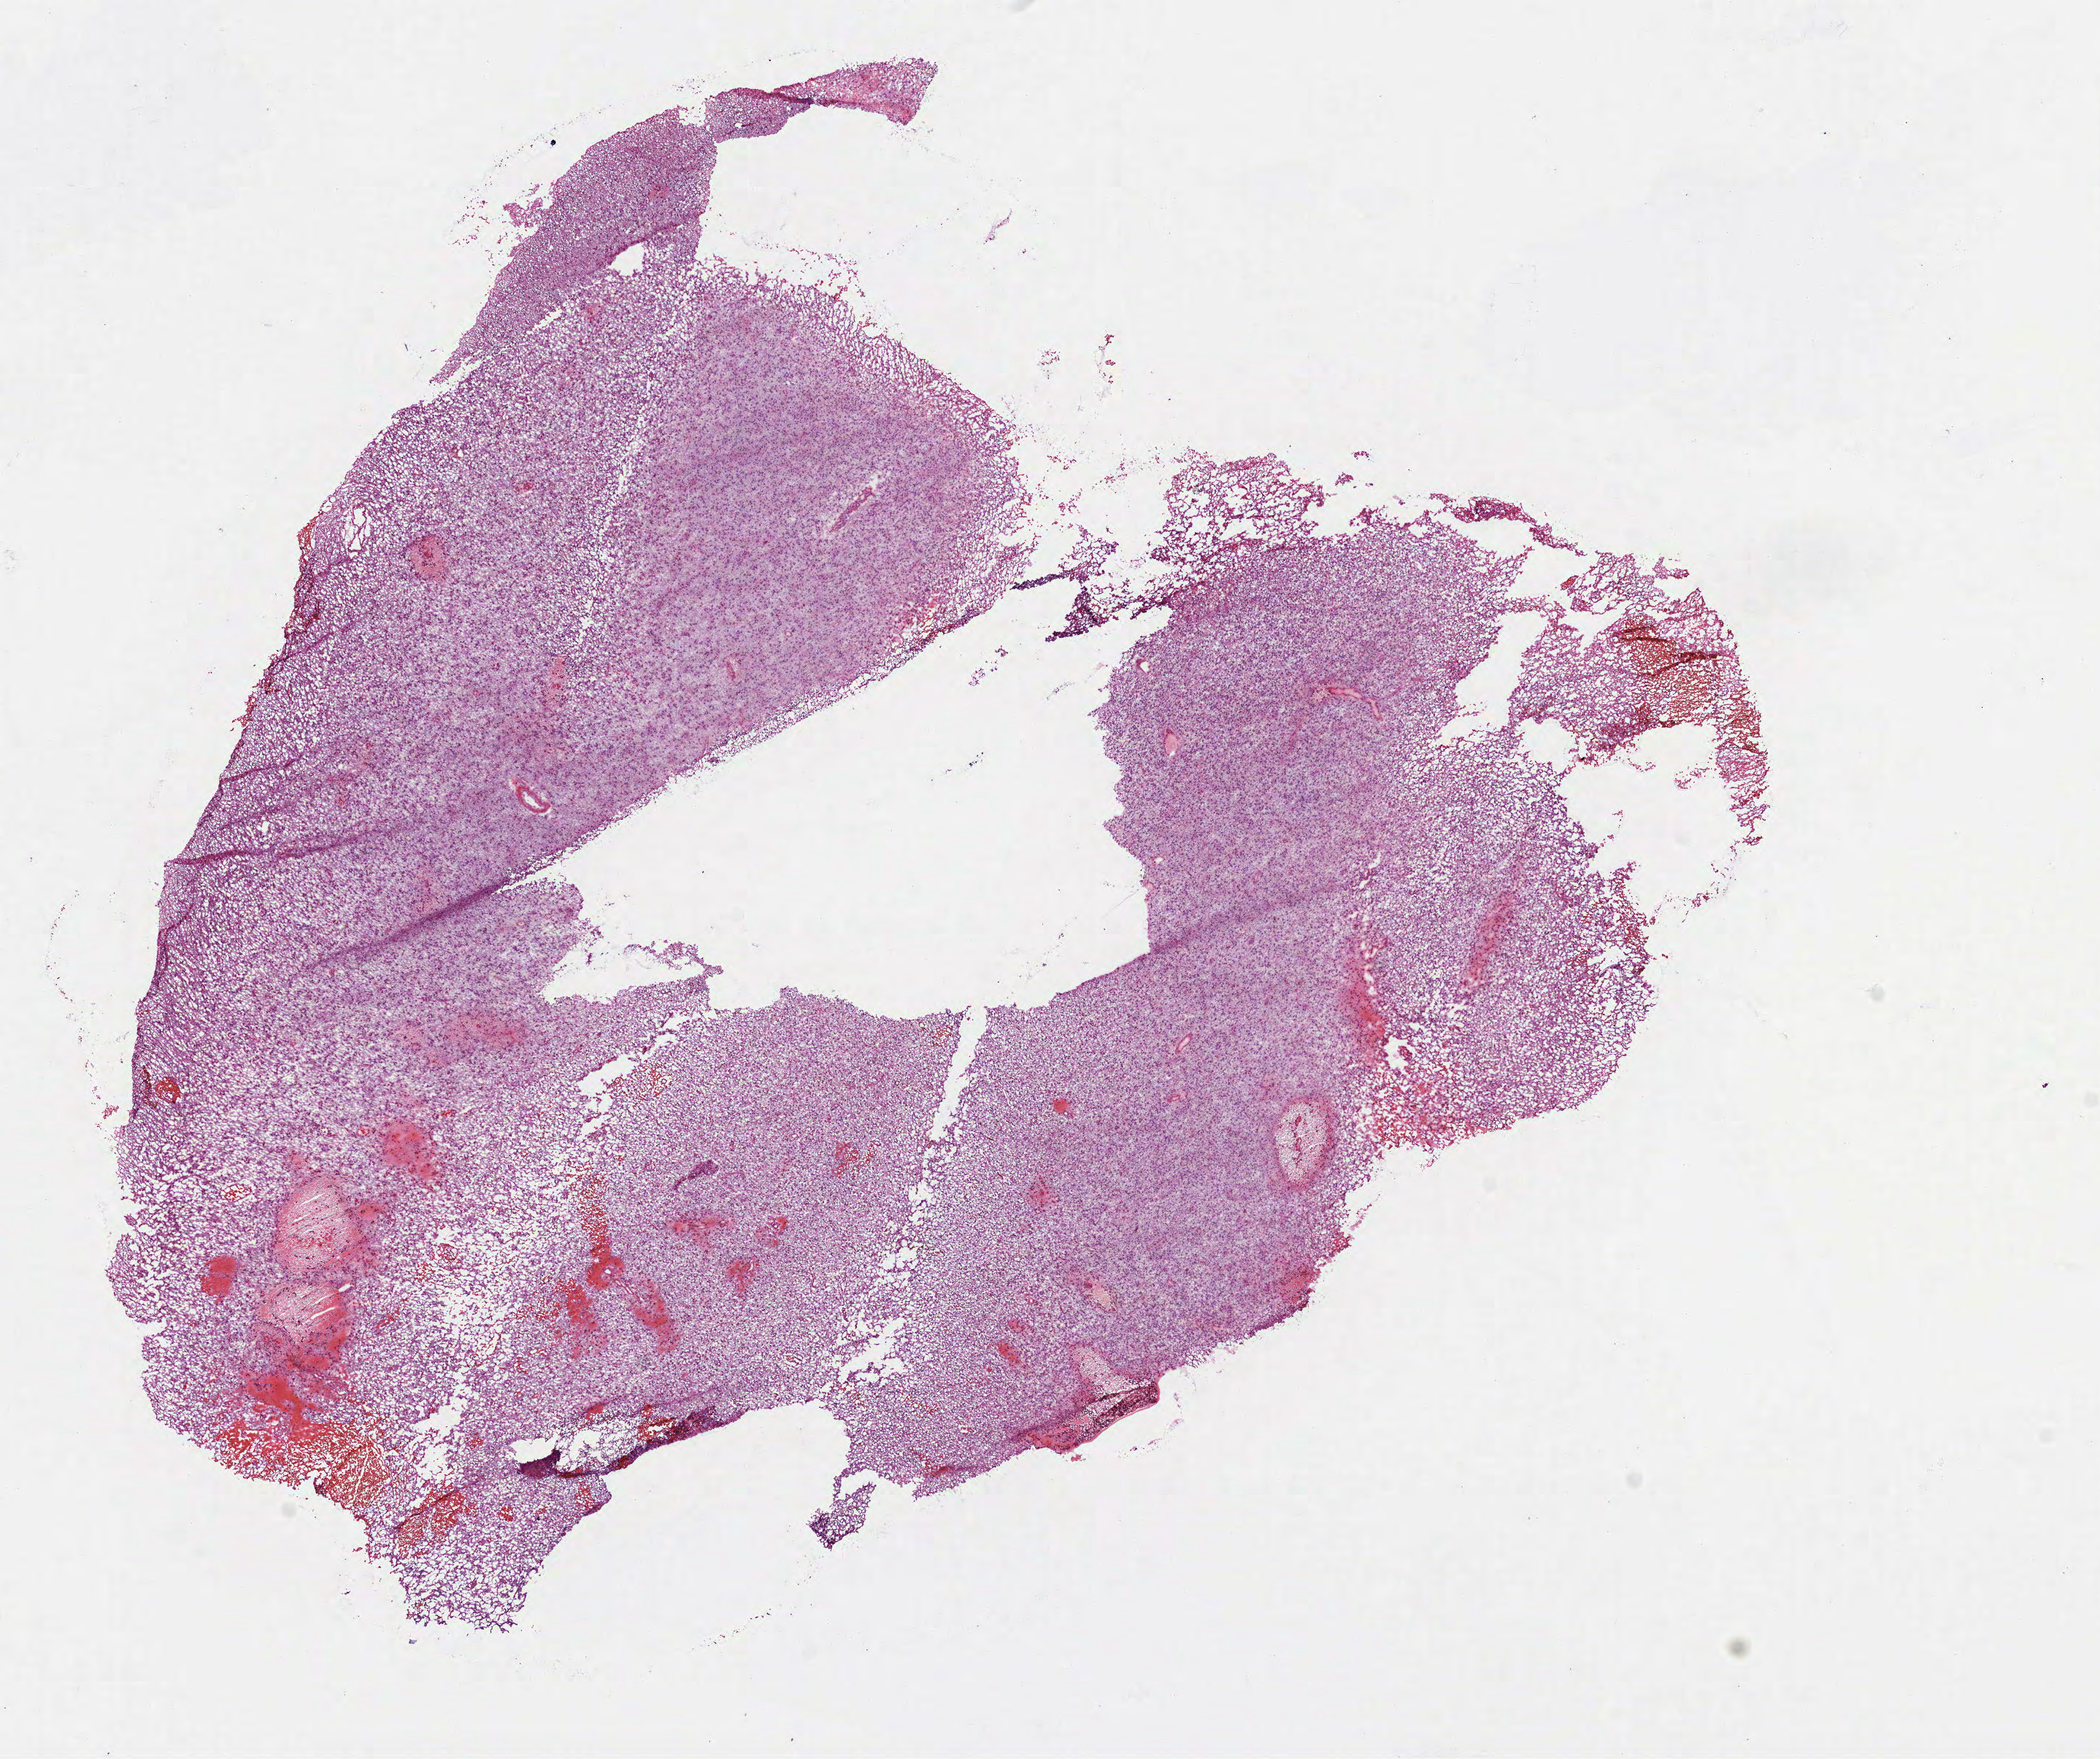
Whole-slide histology image, H&E — whole scanned area (about 11.6 x 9.7 mm, acquisition: 40x scan) shown as a low-resolution overview, frozen section from the bottom of the tissue portion, sample: primary tumour, brain. Female patient; age at initial diagnosis 37 years. Histologic grade: G3 (poorly differentiated). Slide review estimates, as recorded: tumour cells 100%, tumour nuclei 80%, normal cells 0%, stromal cells 0%, necrosis 0%.
Histologic diagnosis: Oligodendroglioma, anaplastic. Laterality: left.